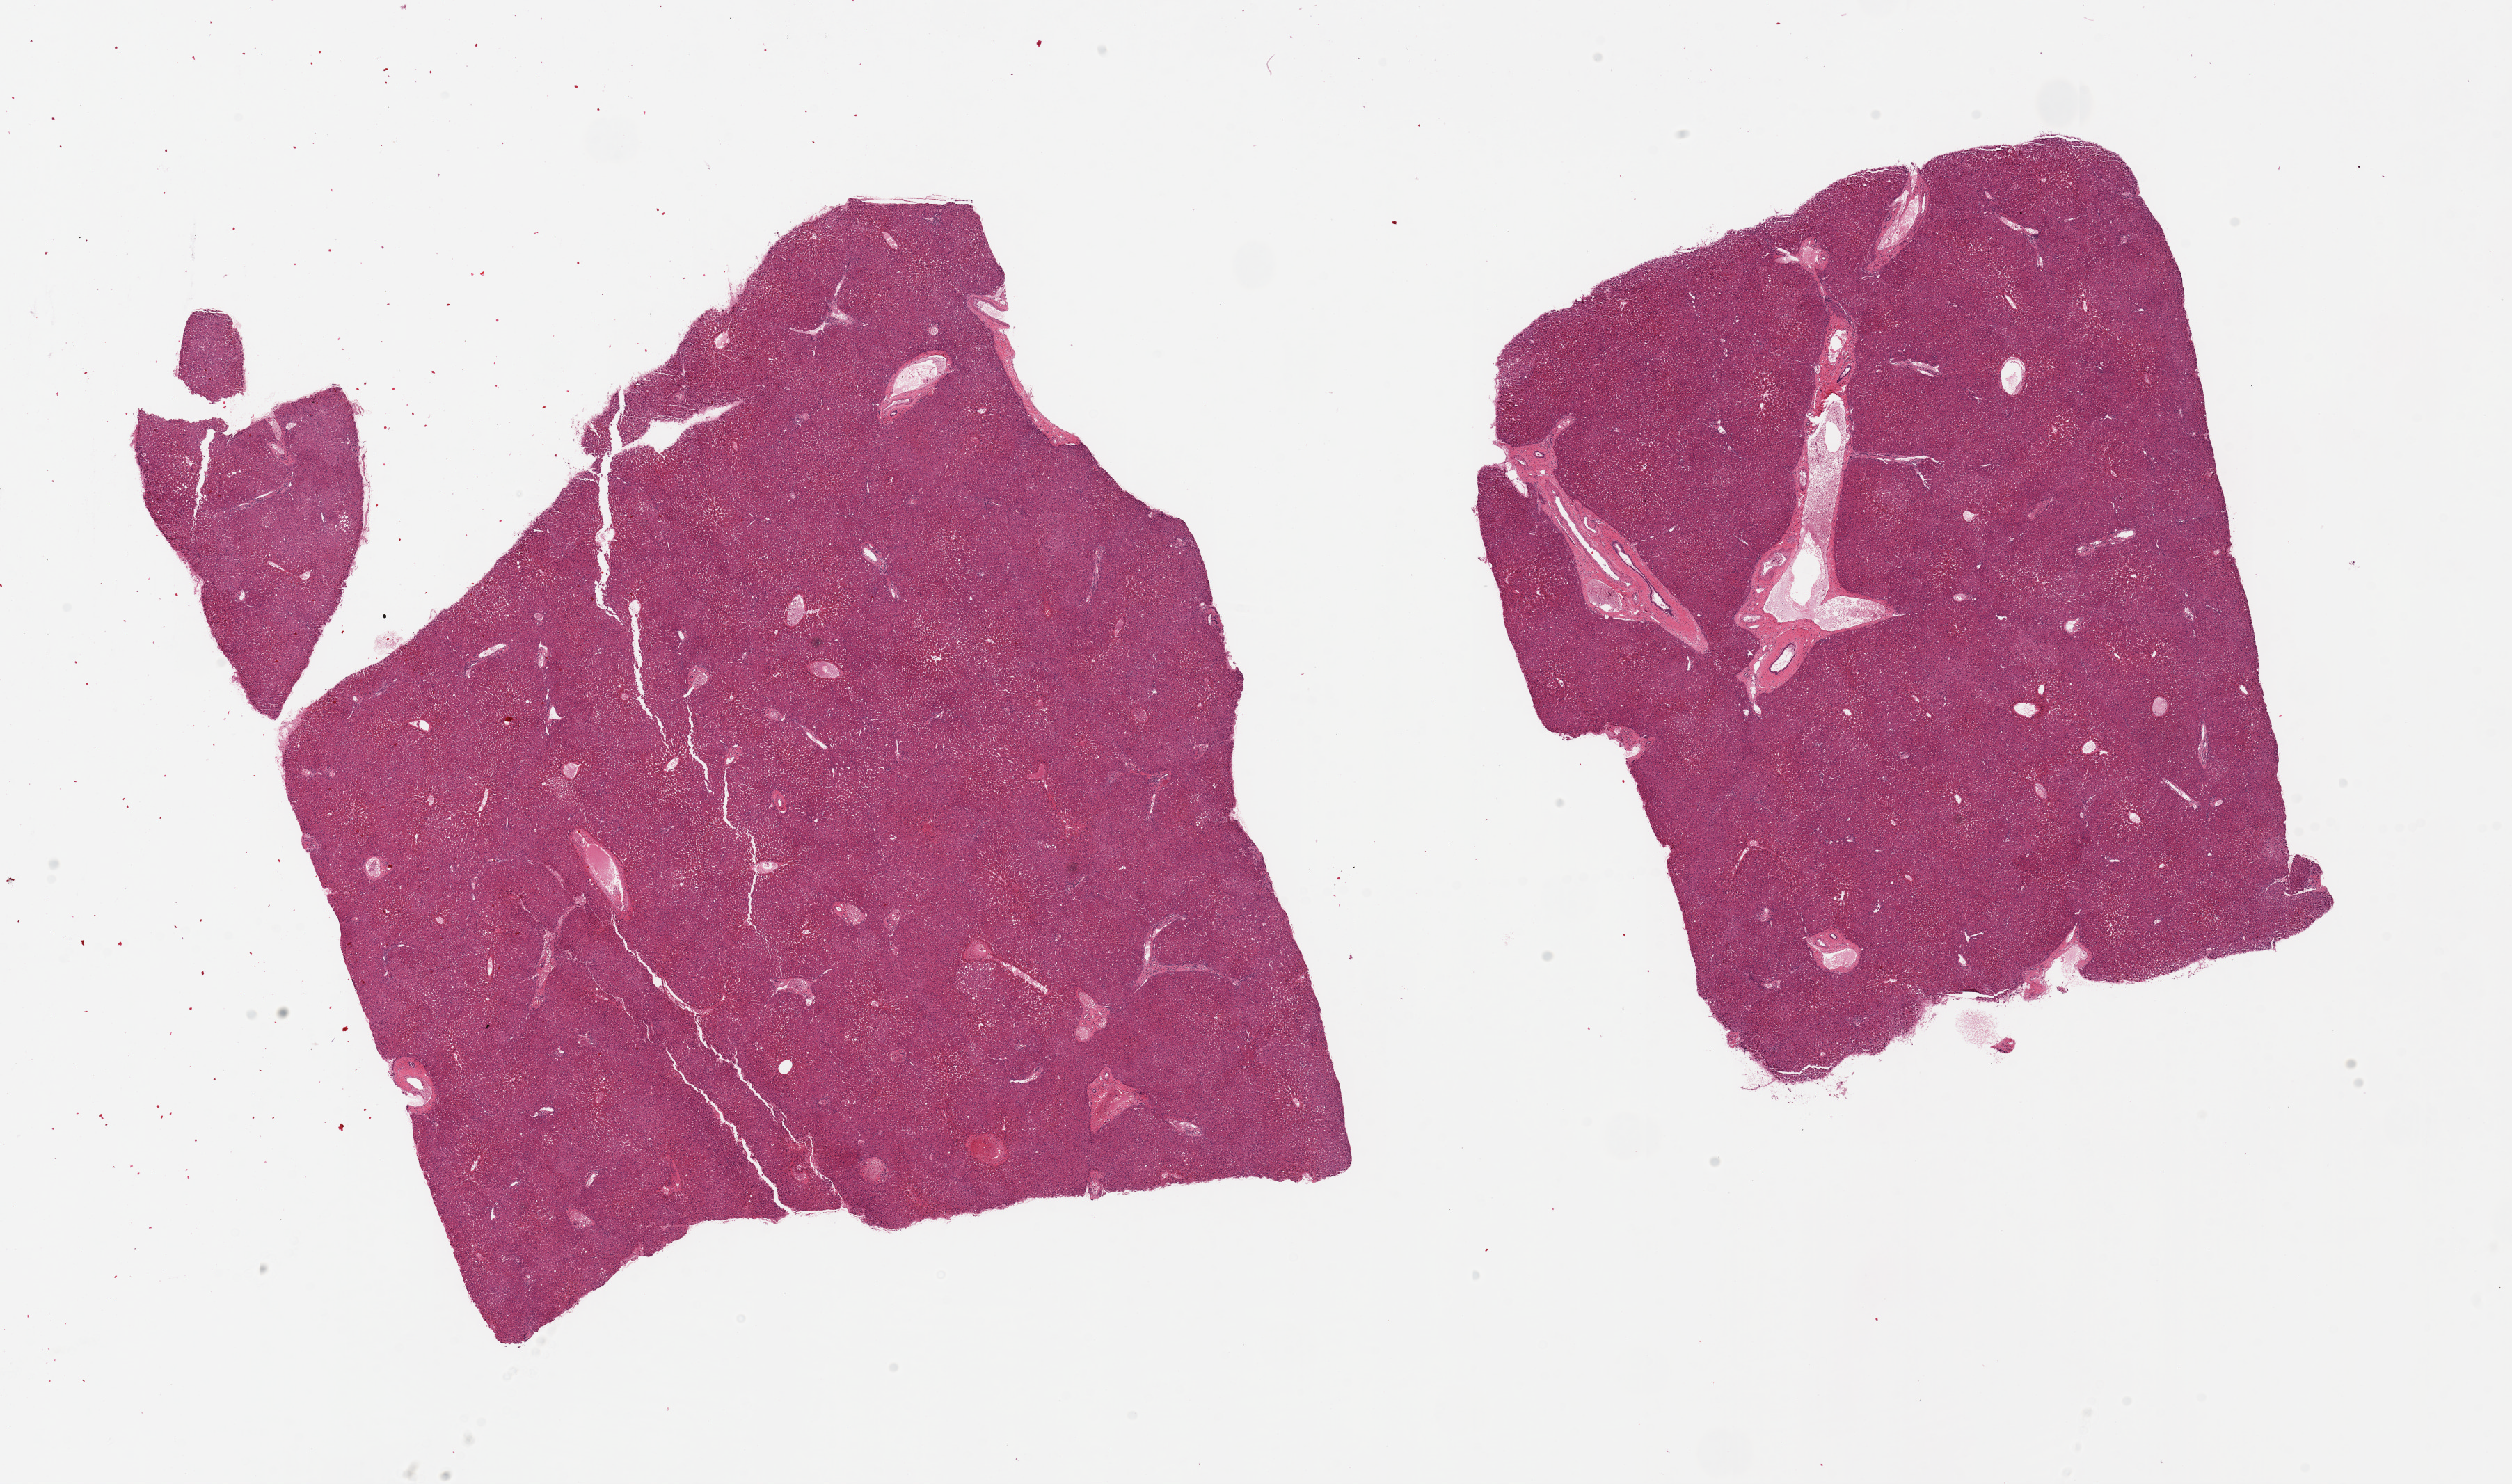
H&E whole-slide image, a low-resolution overview of the entire scanned area, about 28.5 x 16.9 mm; PAXgene-fixed, paraffin-embedded tissue; section of liver (target tissue); donor tissue sample. Donor: male.
Reviewer comment on this tissue sample: 2 pieces, mild steatosis and focal mild portal chronic inflammation.